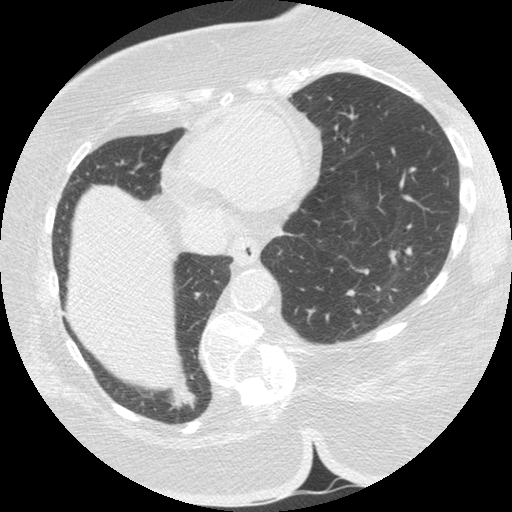
Low-dose screening chest CT, one axial slice; slice 48 of 151 in the series (ordered by position); 140 kVp; lung window (W 1500 / L -600 HU); 512 × 512 image matrix, field of view 340 × 340 mm.
Annotated regions visible in this slice (expert manual segmentation):
- lesion 1 (tumor, lower lobe of right lung): bounding box <170,374,196,410> (left, top, right, bottom; pixels)